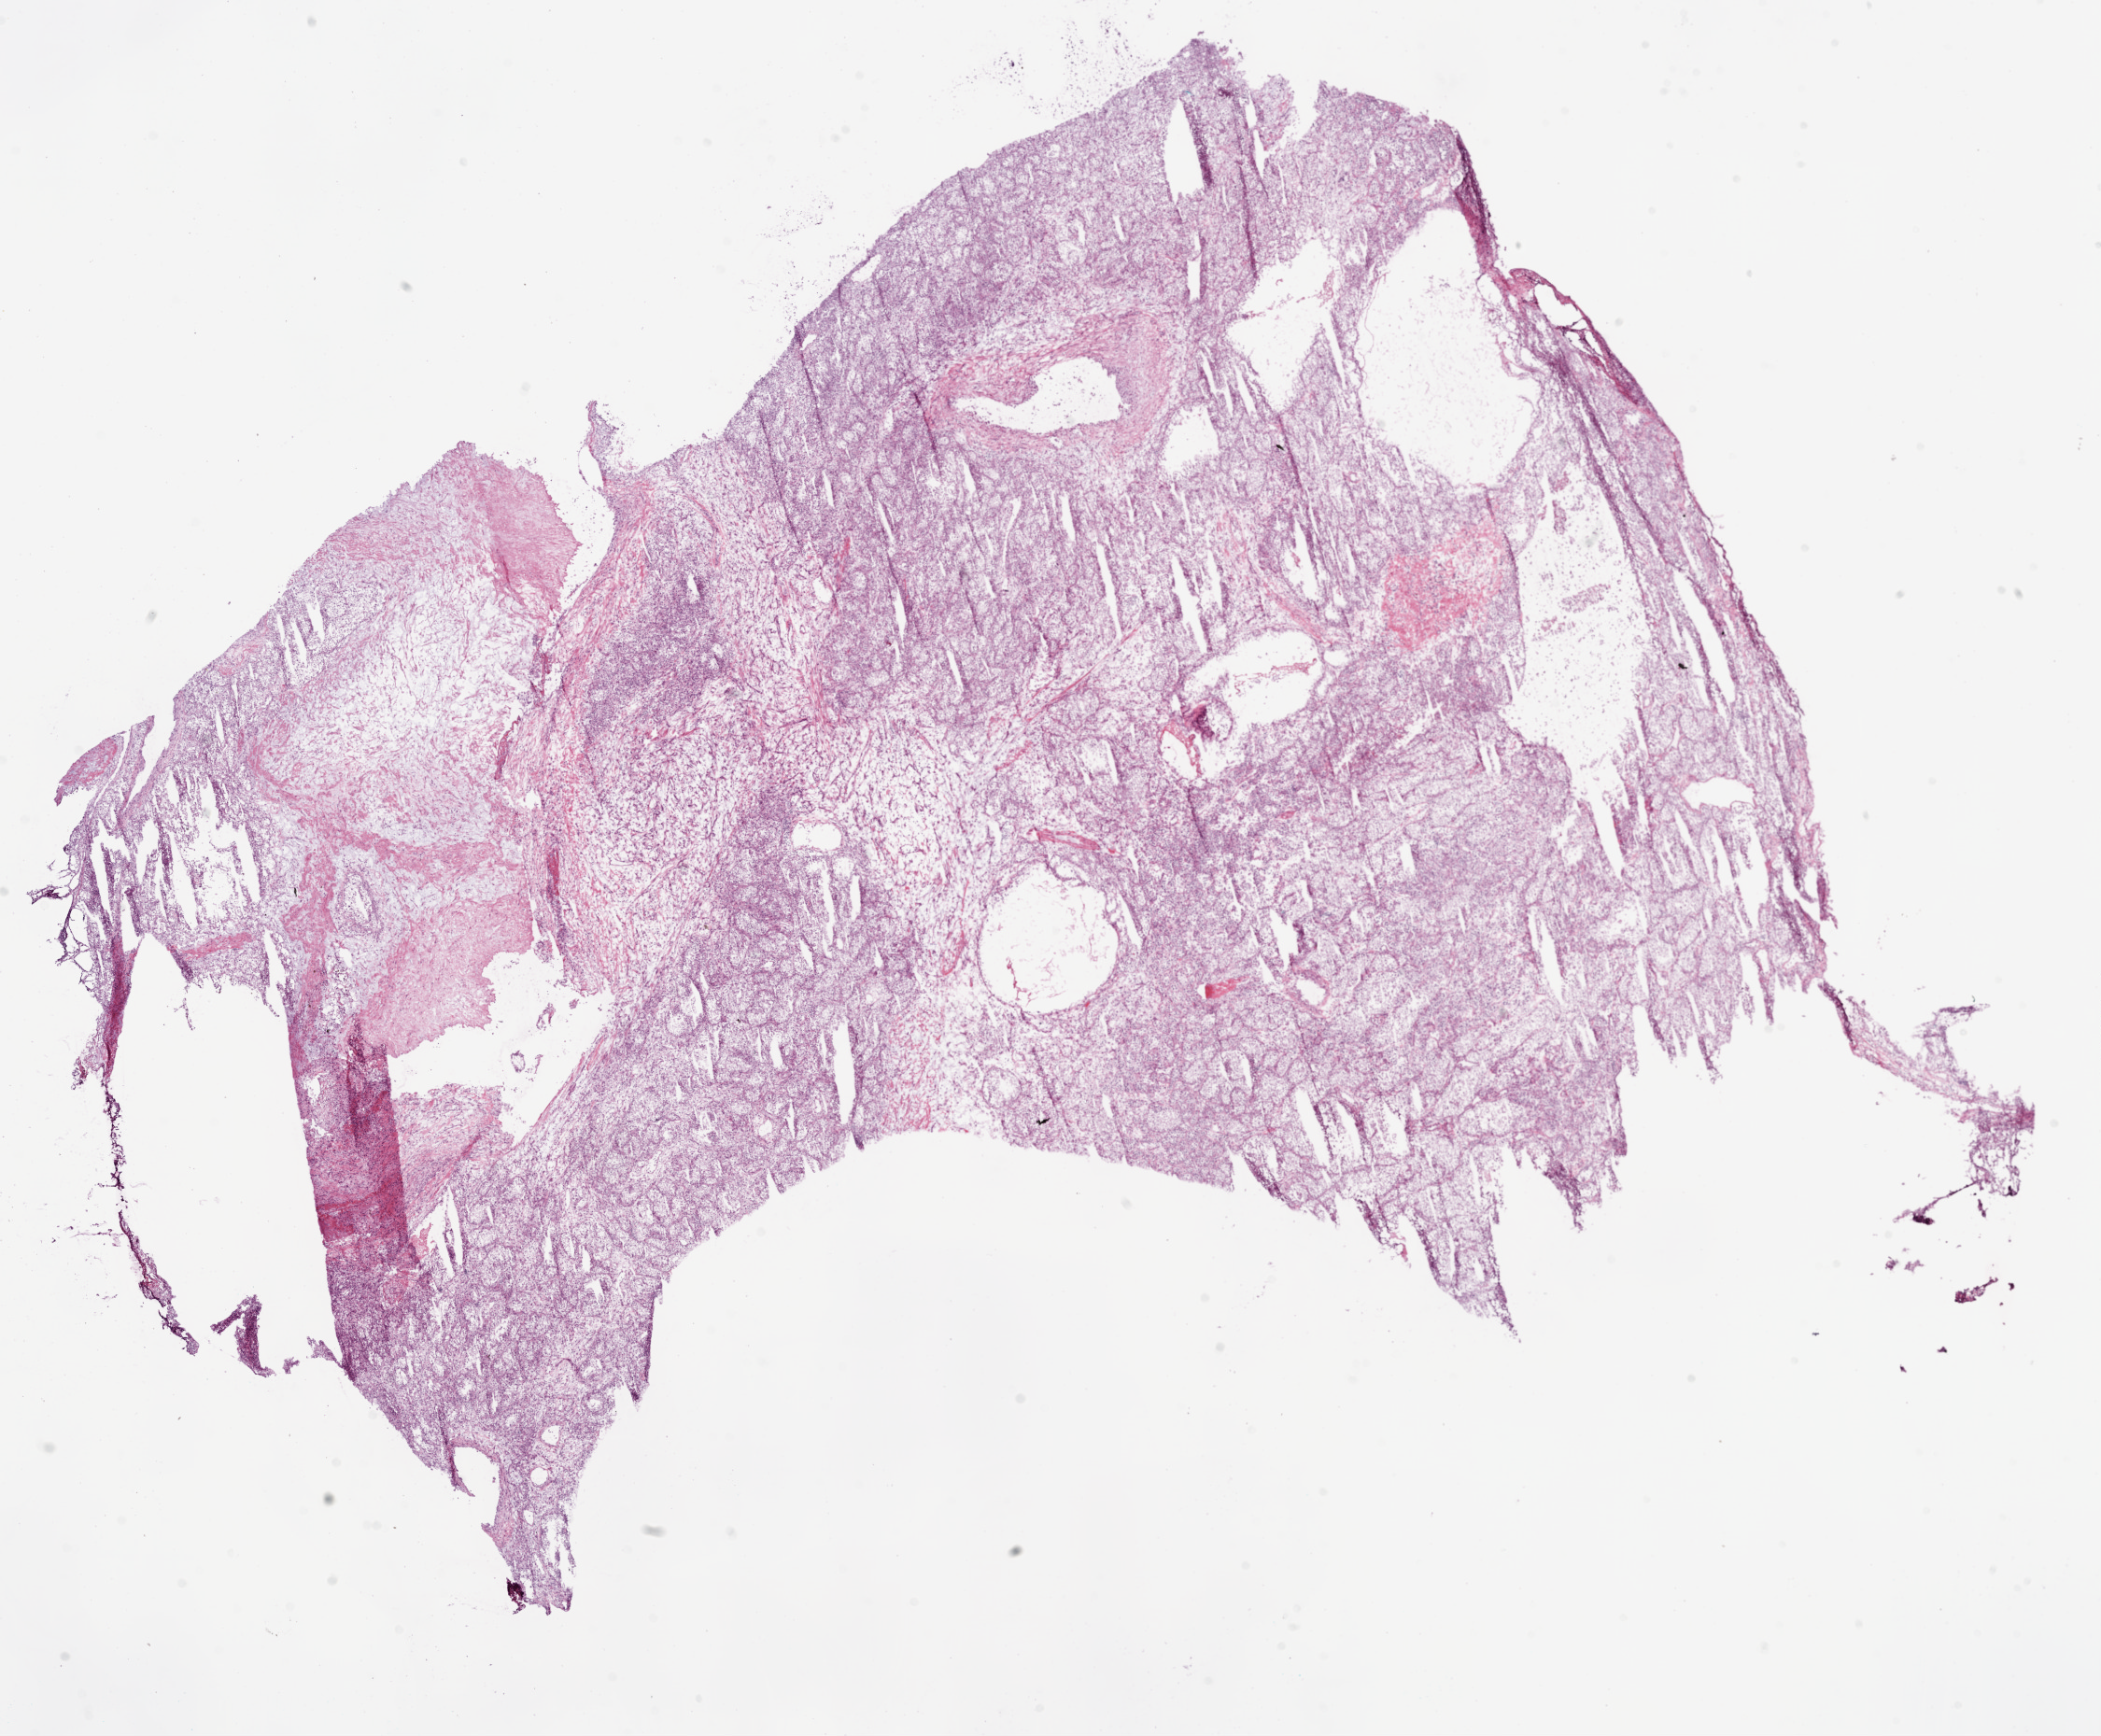
Hematoxylin and eosin (H&E) stained whole-slide image — shown as a low-resolution overview of the whole scanned area (about 18.1 x 14.9 mm); frozen section; sample: primary tumour, kidney. Male, age 57 years at initial diagnosis.
Histologic diagnosis: Clear cell adenocarcinoma, NOS.